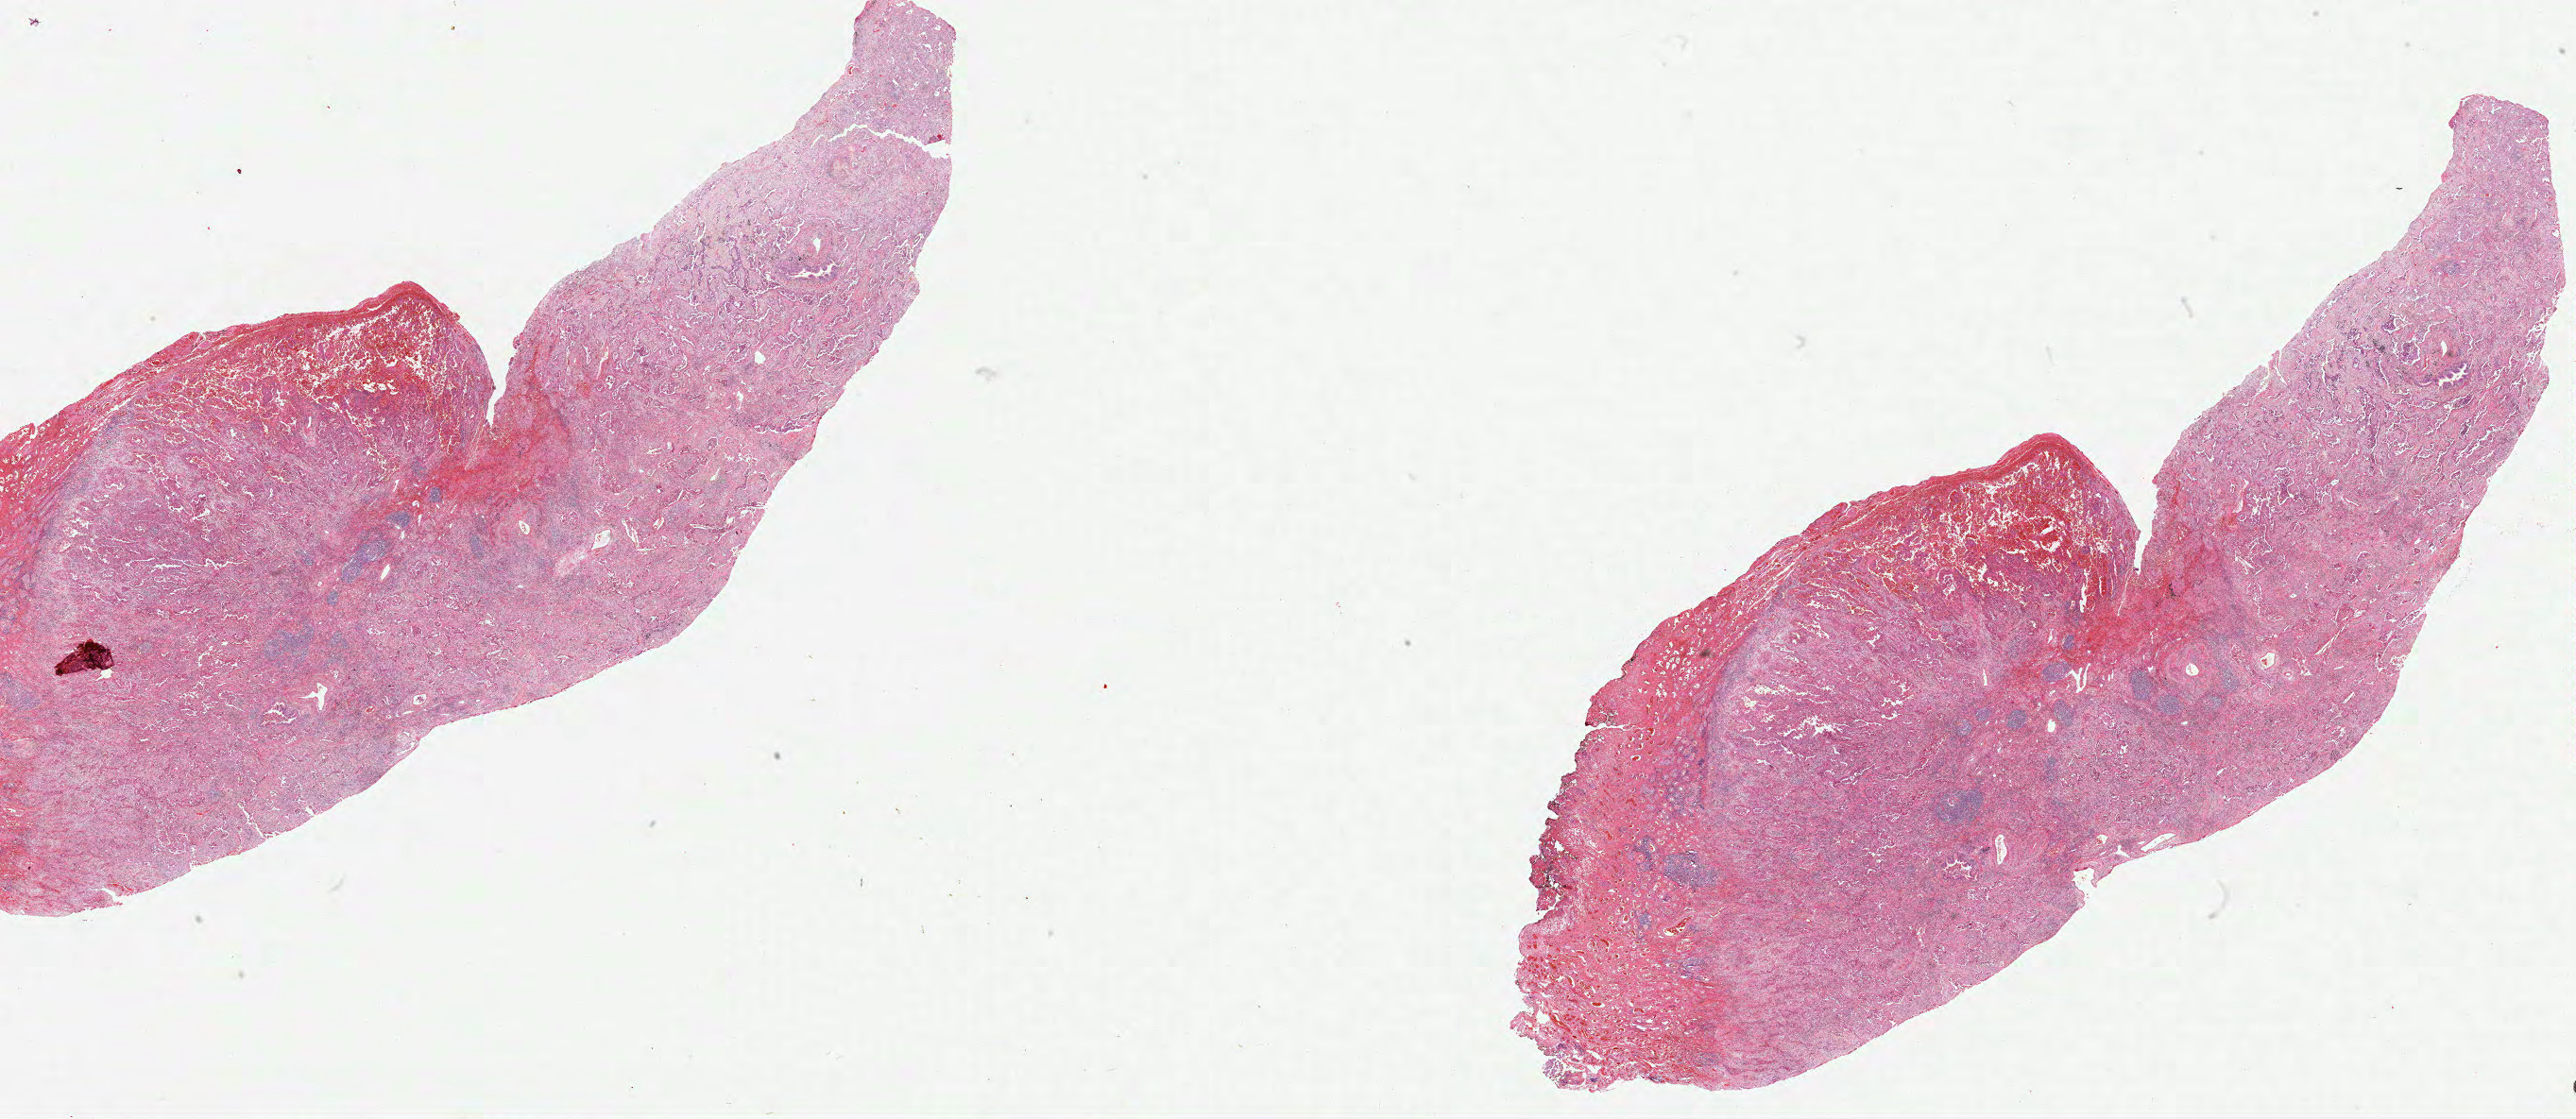
Whole-slide histology image, H&E-stained — whole scanned area (about 44.0 x 19.1 mm, from a 40x scan) shown as a low-resolution overview; FFPE section; lung, primary tumour sample. Patient: female, age at initial diagnosis 80 years.
AJCC pathologic stage: IB (6th edition). Laterality: left. Diagnosis: Adenocarcinoma, NOS (lower lobe, lung).